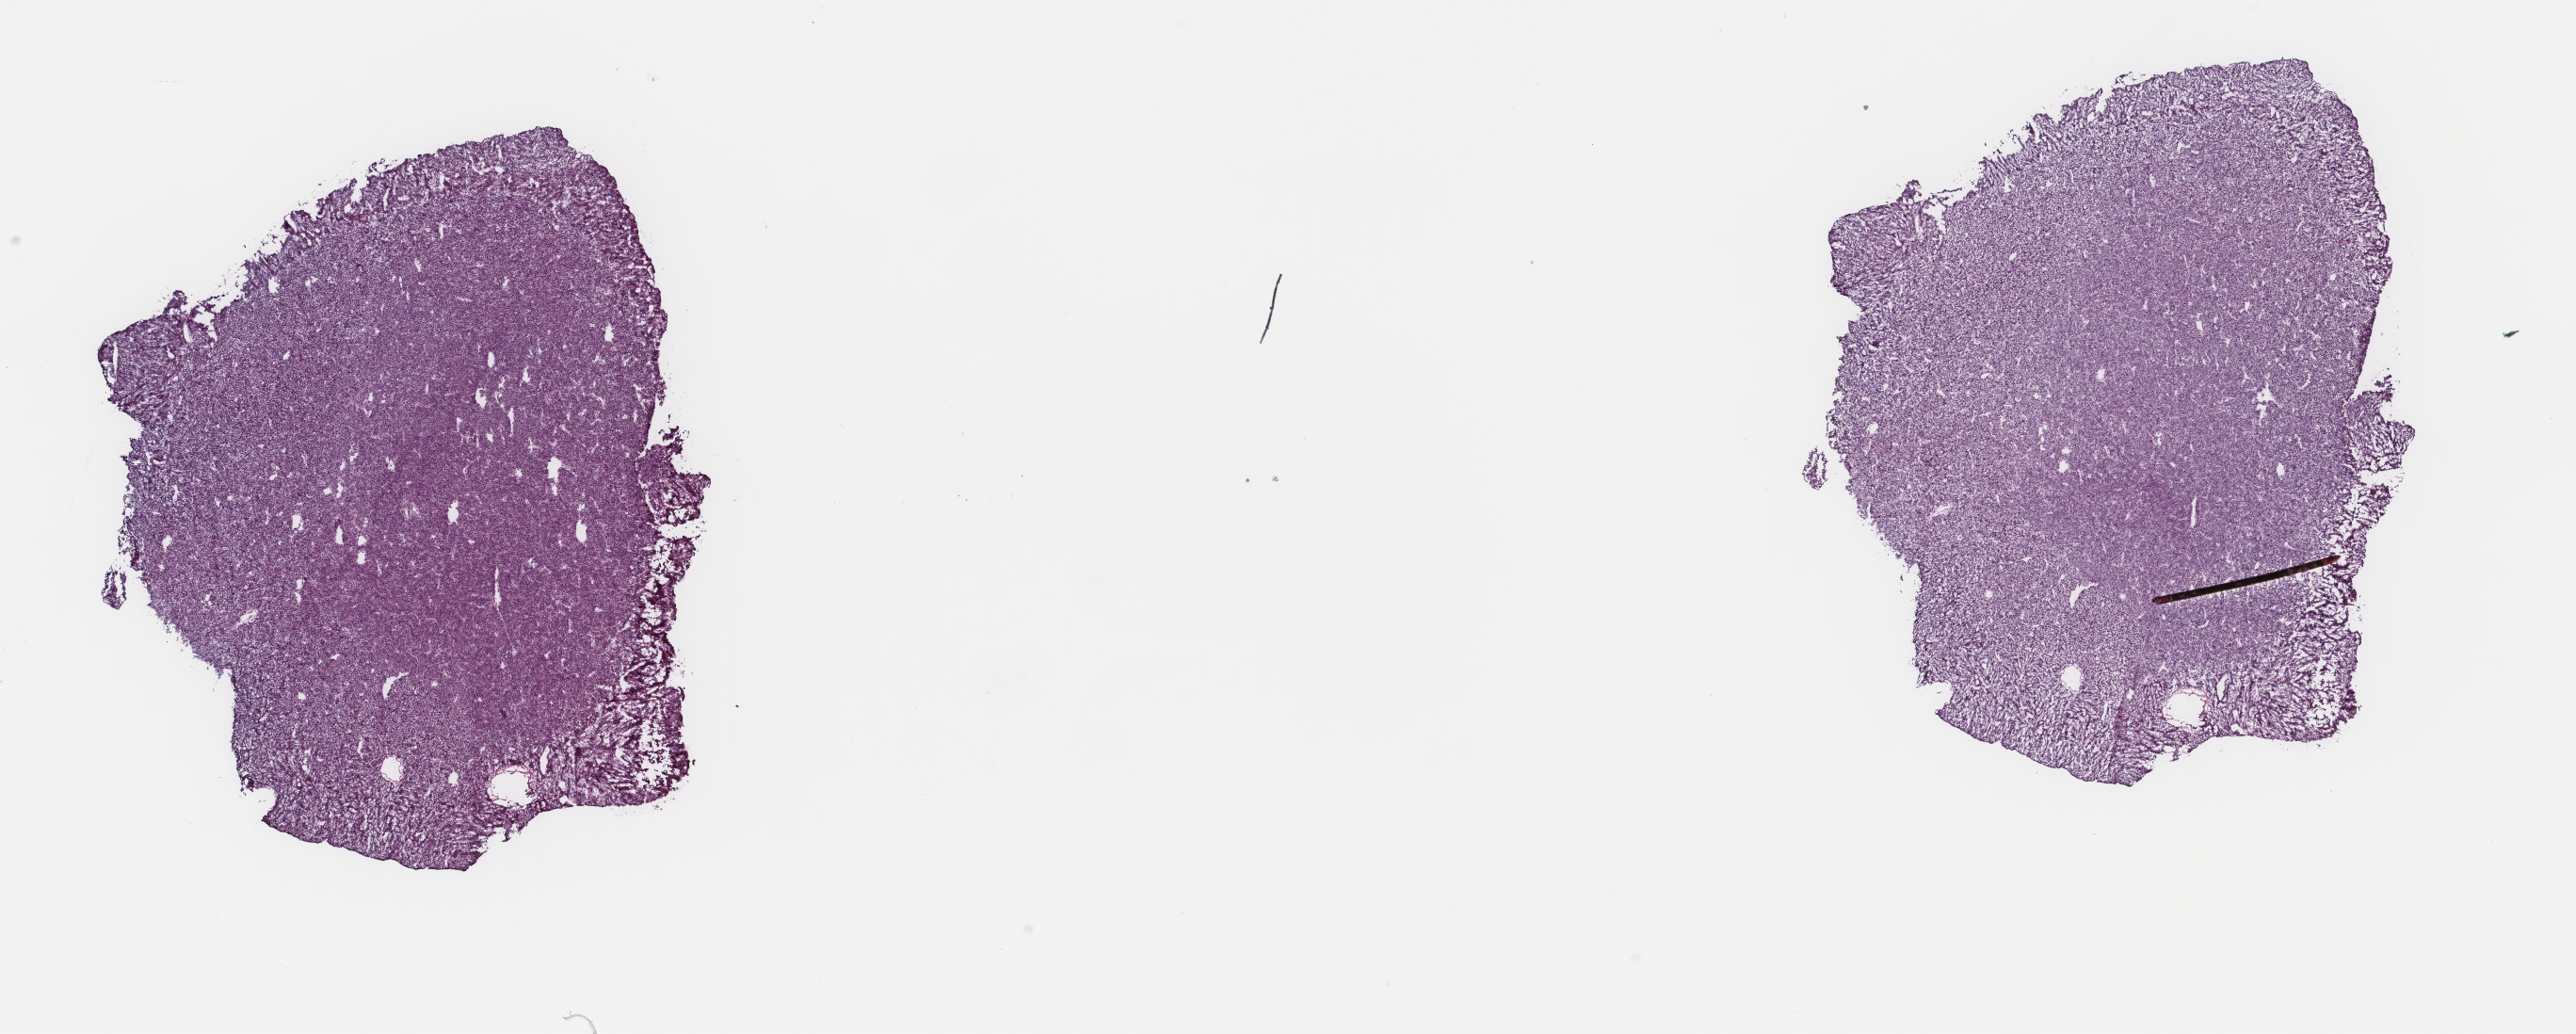
Digitized H&E-stained tissue section (whole slide), a low-resolution overview of the entire scanned area, about 21.7 x 8.7 mm. Frozen section from the top of the tissue portion. Sample: primary tumour, uterus. Female, age 46 years at initial diagnosis. Composition of this section per pathologist review: tumour cells 85%, tumour nuclei 100%, normal cells 0%, stromal cells 15%, necrosis 0%. Infiltration values recorded for this section: lymphocyte infiltration 0%, monocyte infiltration 0%, neutrophil infiltration 0%.
Pathologic diagnosis: Leiomyosarcoma, NOS.